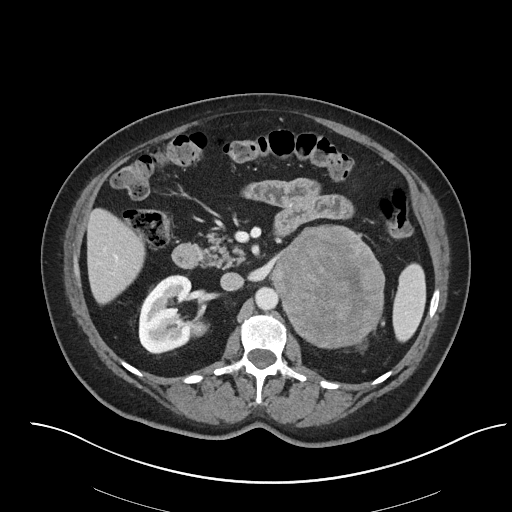
Contrast-enhanced abdominal CT, one axial slice. Slice 39 of 92 in the series (ordered by position). Reconstruction kernel I40f/2. Intravenous contrast given. Soft-tissue window (W 400 / L 40 HU). 512 × 512 image matrix. Female patient, age 53 years. From the clinical record (not read from this slice): diagnosis: adrenocortical carcinoma; tumour side: left adrenal; tumour size at pathology: 9 cm; Ki-67 index: 28 %; stage (as recorded): 2.
Structures marked on this image (semi-automatic segmentation, software-assisted and operator-edited):
- mass: bounding box <272,226,384,346> (left, top, right, bottom; pixels)